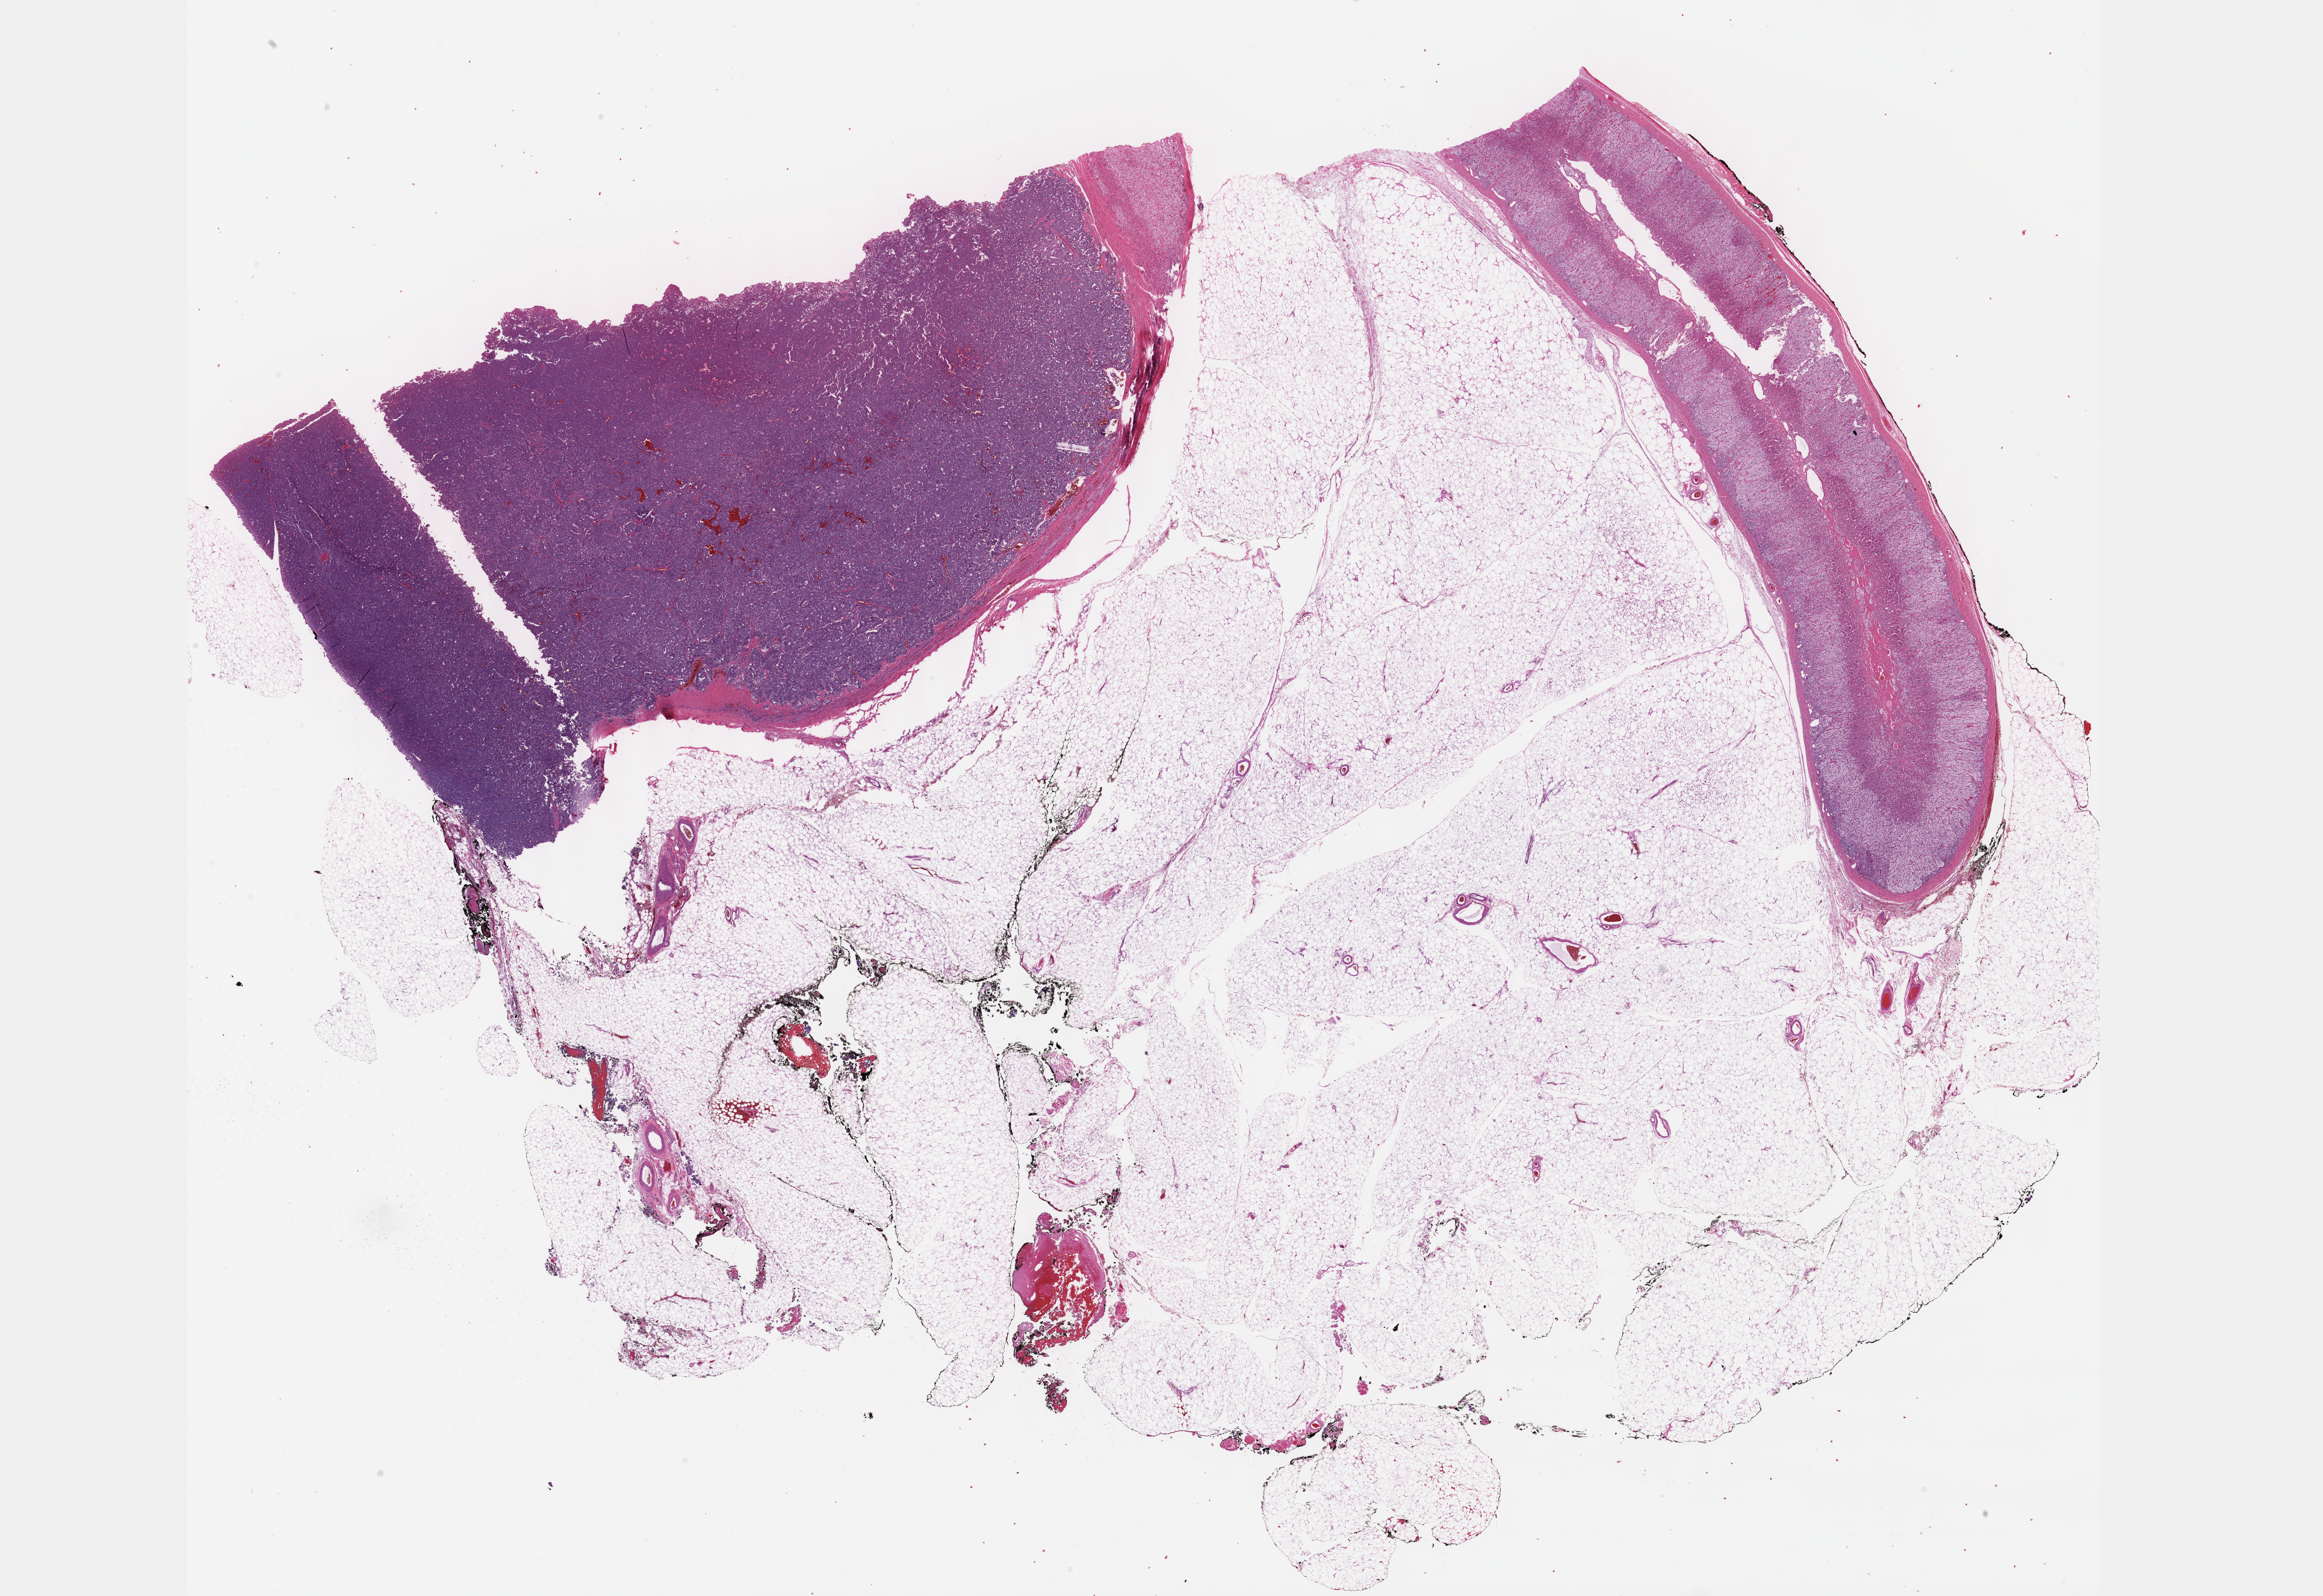
H&E whole-slide image, whole scanned area (about 31.2 x 21.4 mm, slide scanned at 40x) shown as a low-resolution overview; formalin-fixed paraffin-embedded (FFPE) diagnostic section; adrenal gland, primary tumour sample. Male, age 40 years at initial diagnosis.
* pathologic diagnosis: Pheochromocytoma, NOS